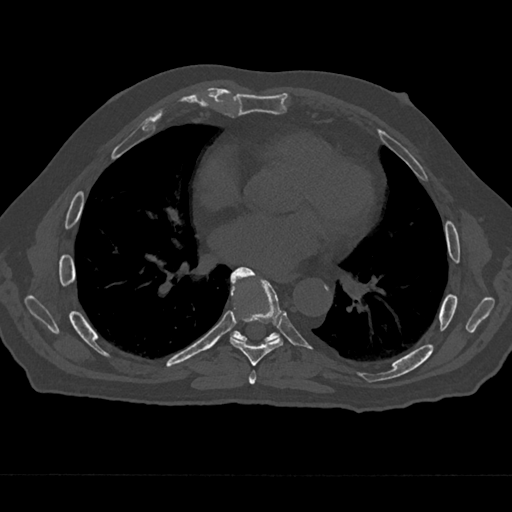
CT including the spine, one axial slice; reconstruction kernel Br40s/3; 120 kVp; bone window (W 1800 / L 400 HU); 512 × 512 image matrix, field of view 377 × 377 mm. Male patient, age 75 years. From the clinical record (not read from this slice): primary cancer: renal; vertebrae with lytic lesions (as recorded): T4.
Structures marked on this image (semi-automatic segmentation, software-assisted and operator-edited):
- T6 vertebra: bounding box (x1, y1, x2, y2) in pixels: (249, 371, 256, 385)
- T7 vertebra: (230, 267, 283, 366)
- T8 vertebra: (230, 279, 280, 342)